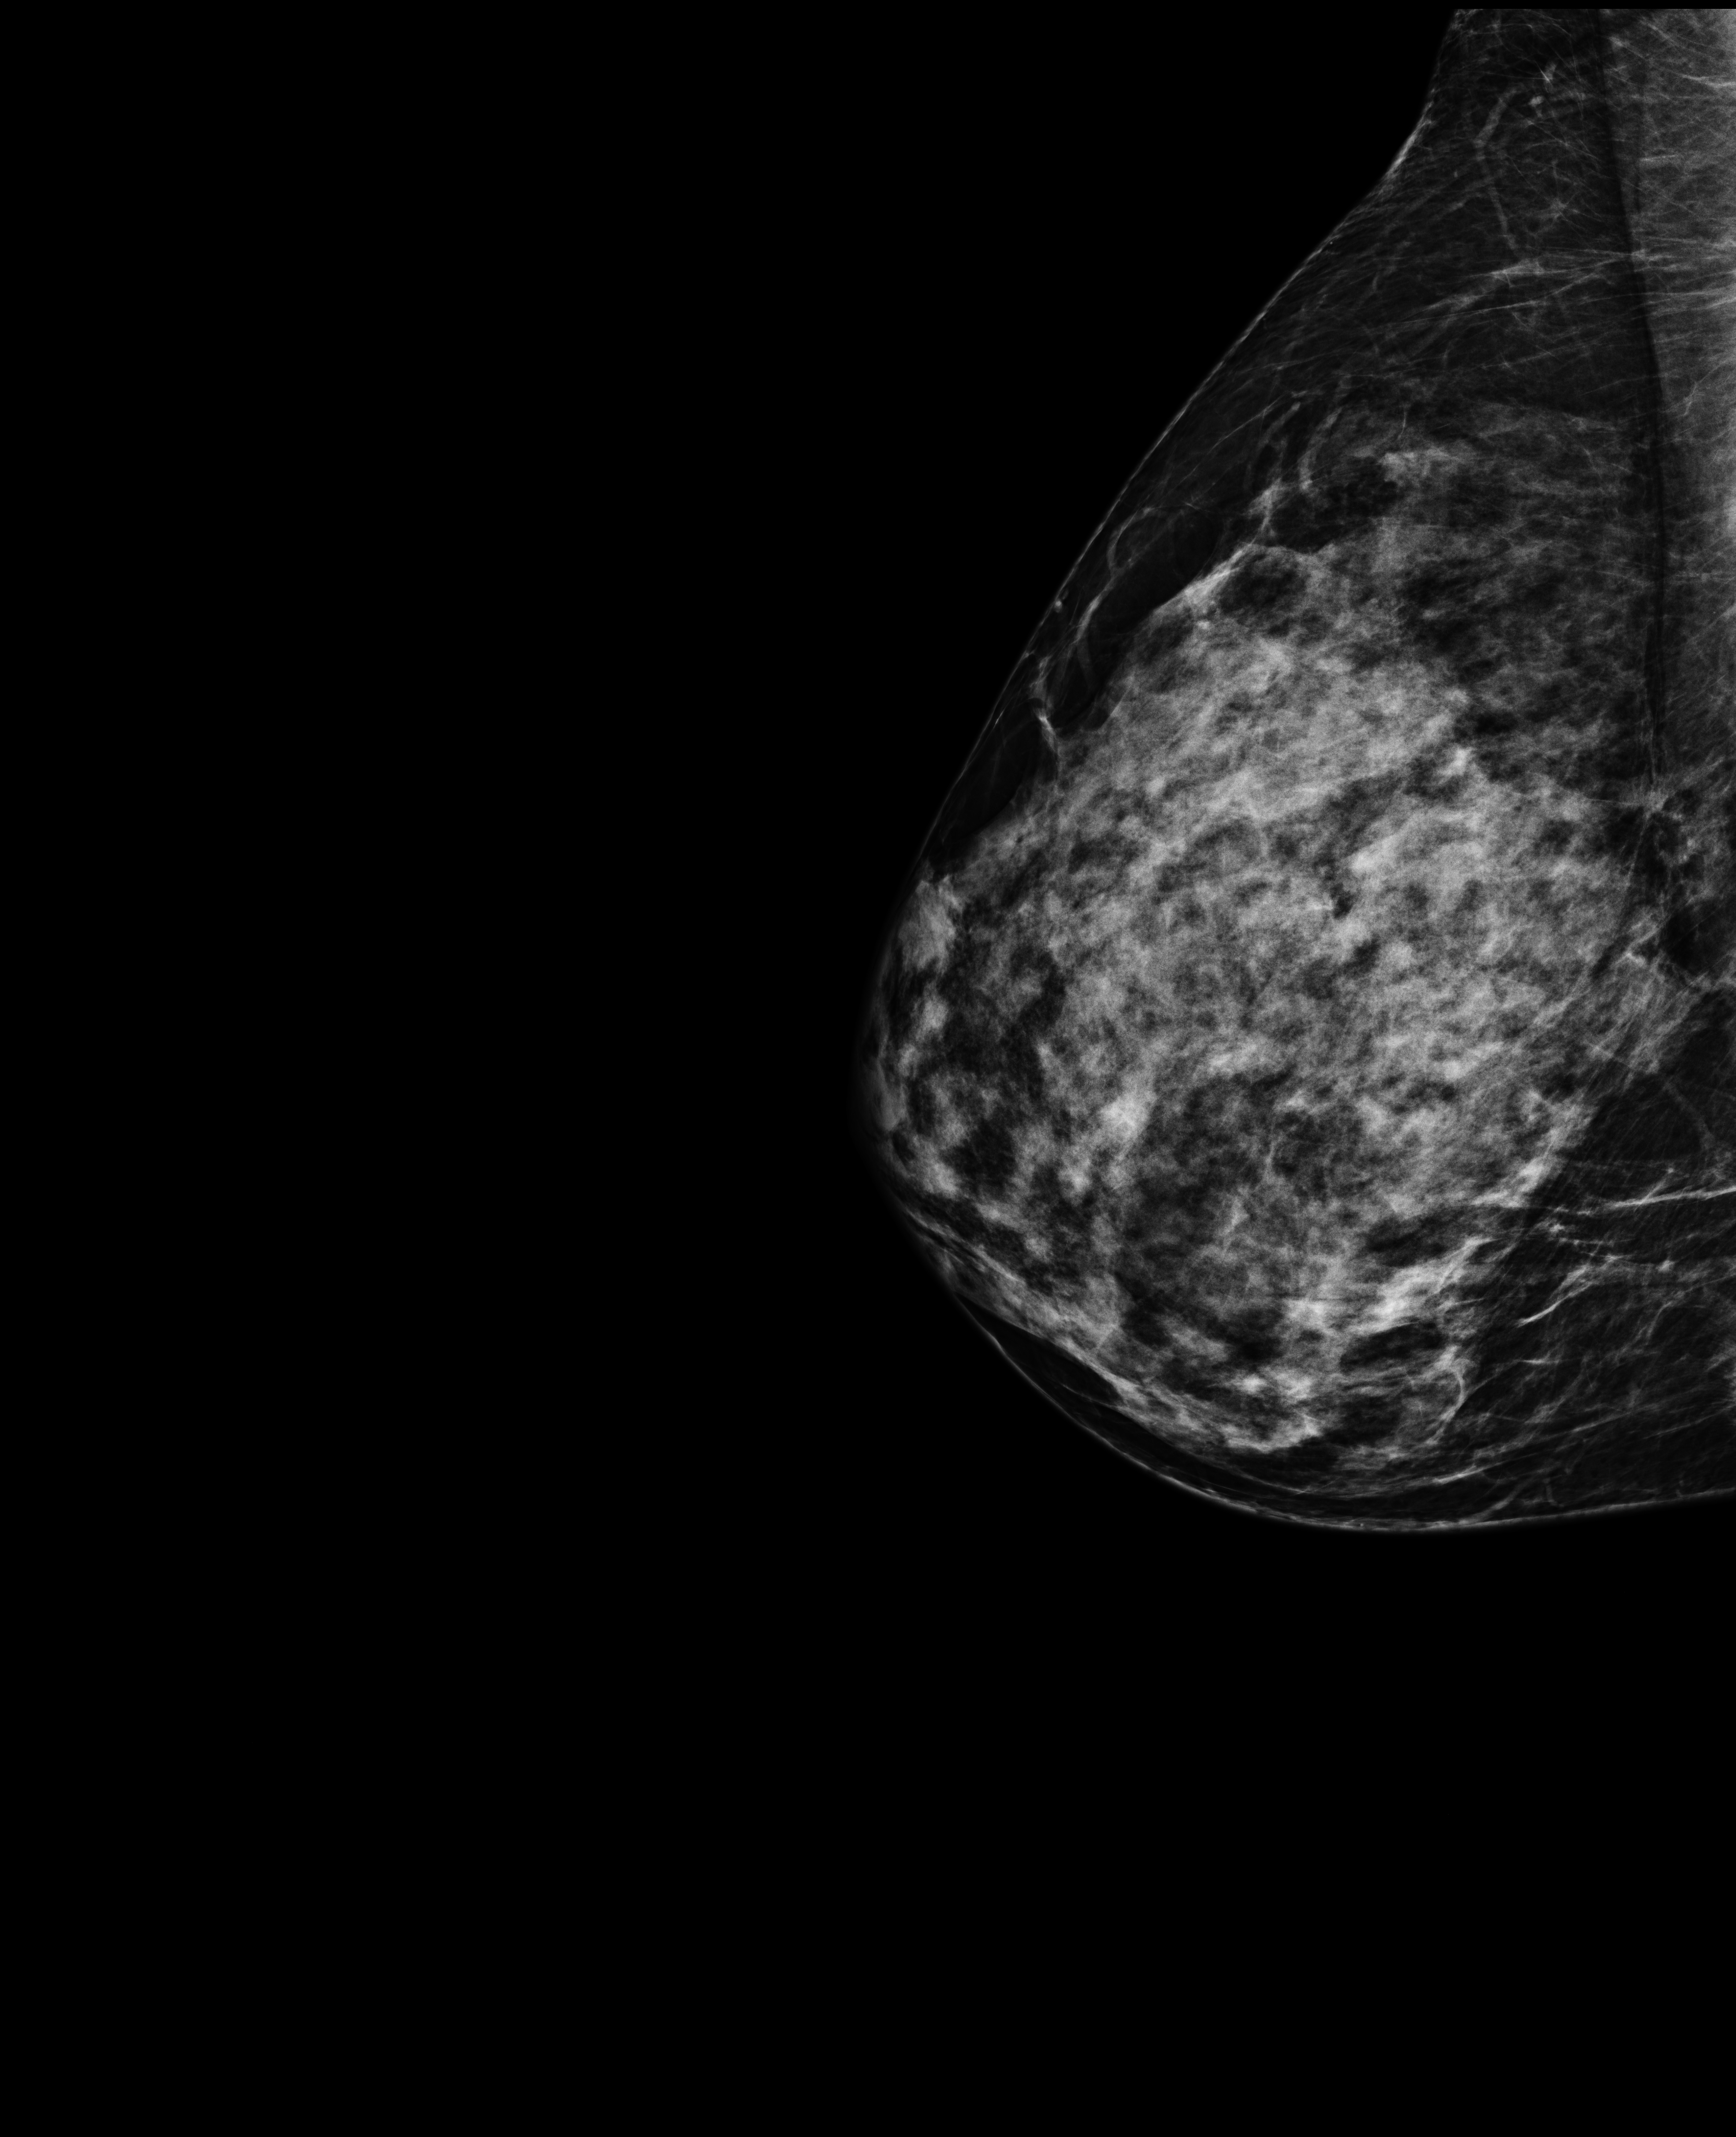
Annual screening mammography examination, compressed breast thickness 77 mm. Patient: female, 43 years.
Image type: full-field digital mammogram. Breast: right. Projection: laterally exaggerated craniocaudal (XCCL) view.